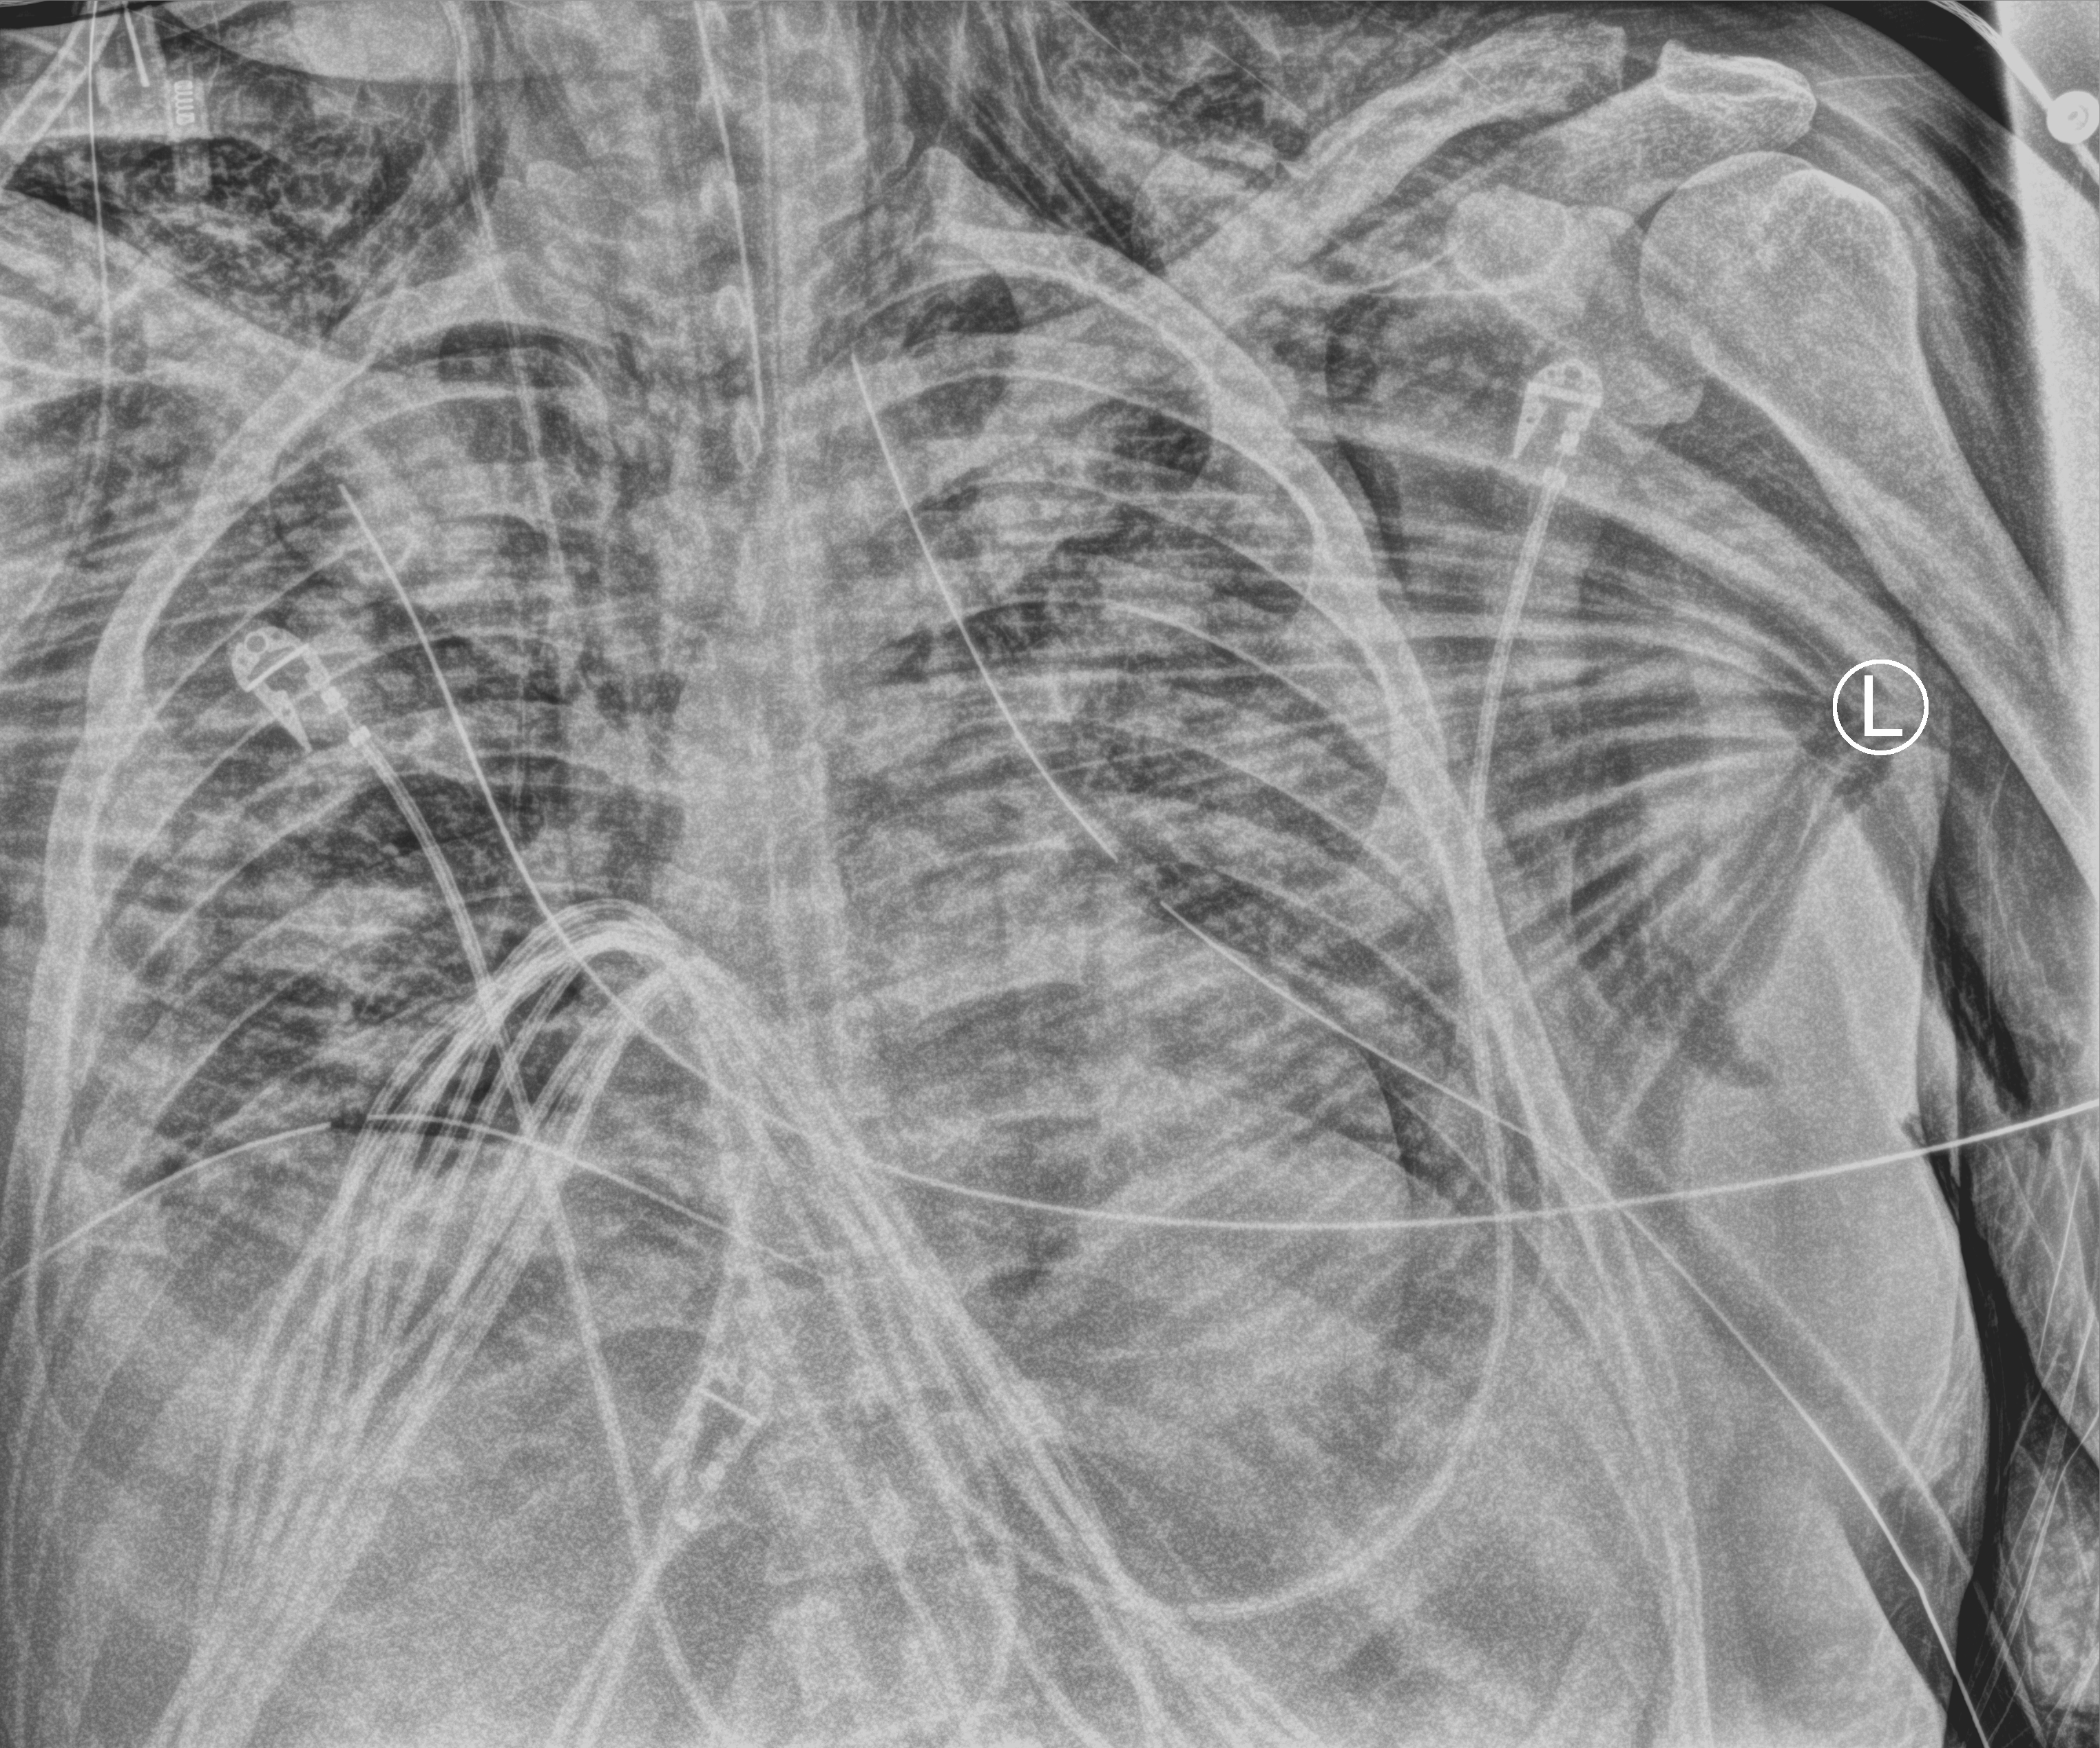
Bedside chest radiograph (computed radiography); anteroposterior (AP) projection. Patient hospitalised with COVID-19; male, aged 18–59 years.
Hospital-stay facts (about this admission, not read from this image; timing relative to this image not recorded): mechanically ventilated during this hospital stay: yes; admitted to intensive care during this hospital stay: yes.